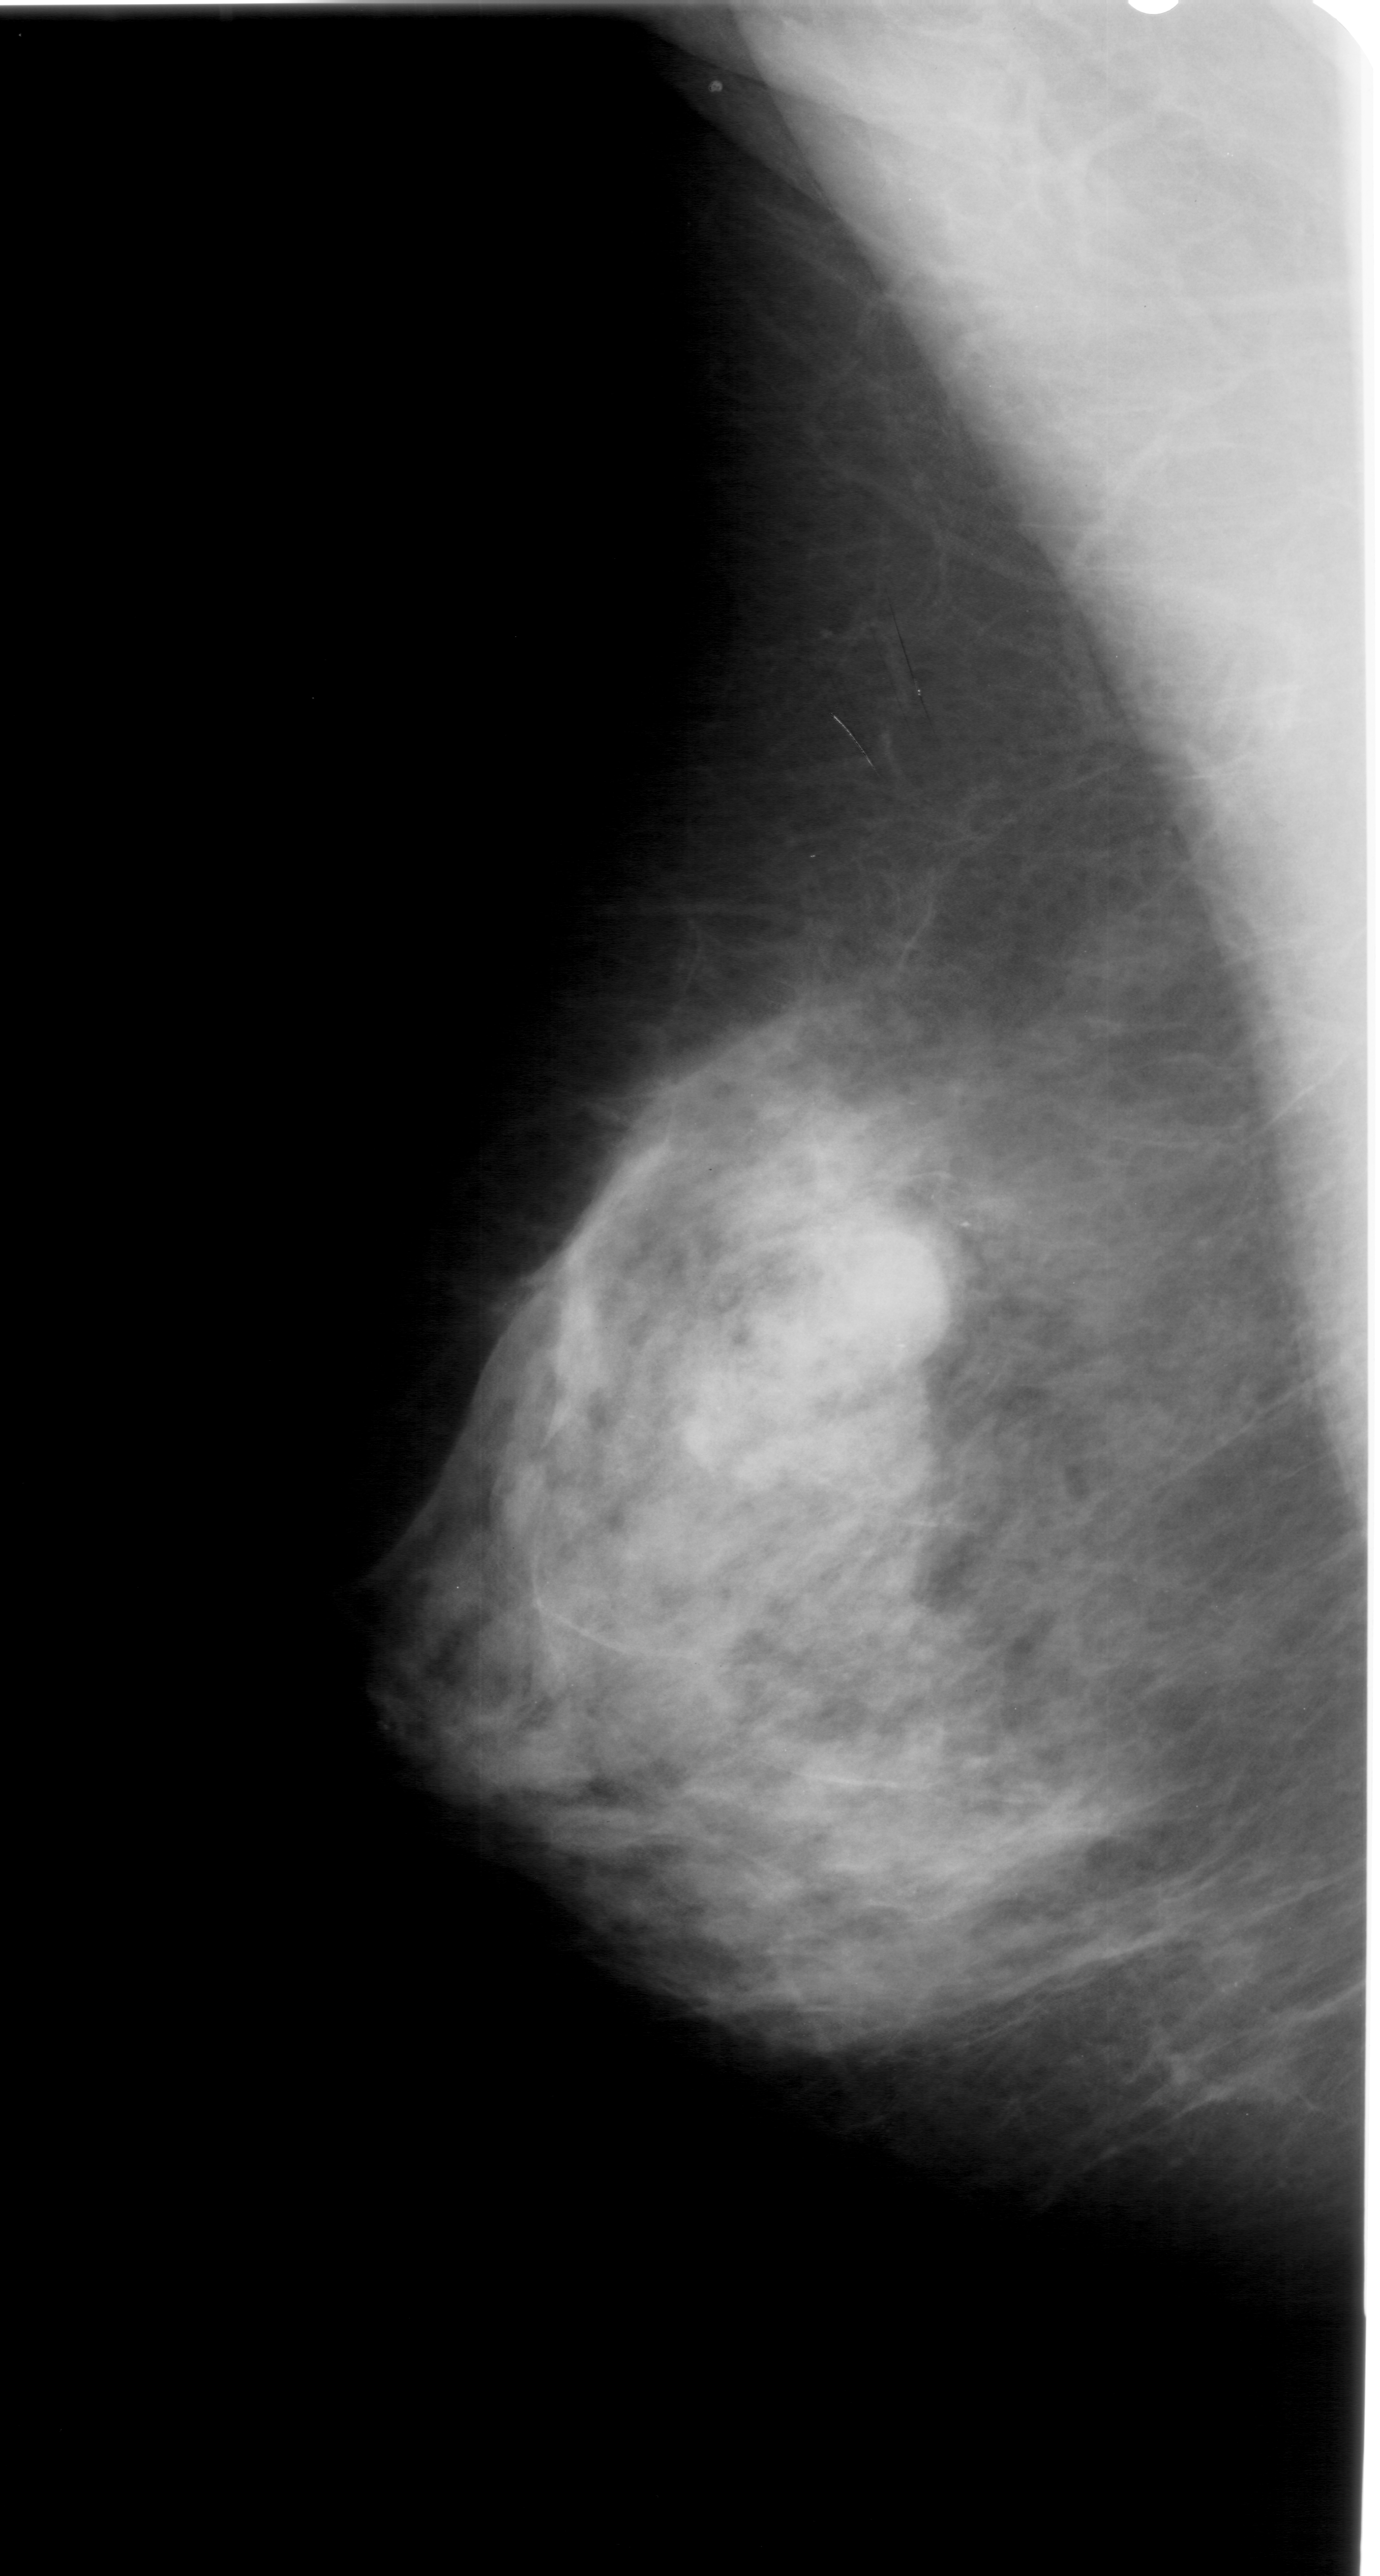
Mammogram (digitized film); left breast; mediolateral oblique (MLO) view; BI-RADS breast density category 4 (scale 1–4); 1380 × 2576 image matrix.
Expert-marked regions of interest on this image (one box per marked abnormality):
- mass, shape round, margins obscured; BI-RADS assessment category 4; subtlety rating 3 on a 1 (subtle) to 5 (obvious) scale; pathology (as recorded): benign: box from (x=786, y=1198) to (x=968, y=1384) px